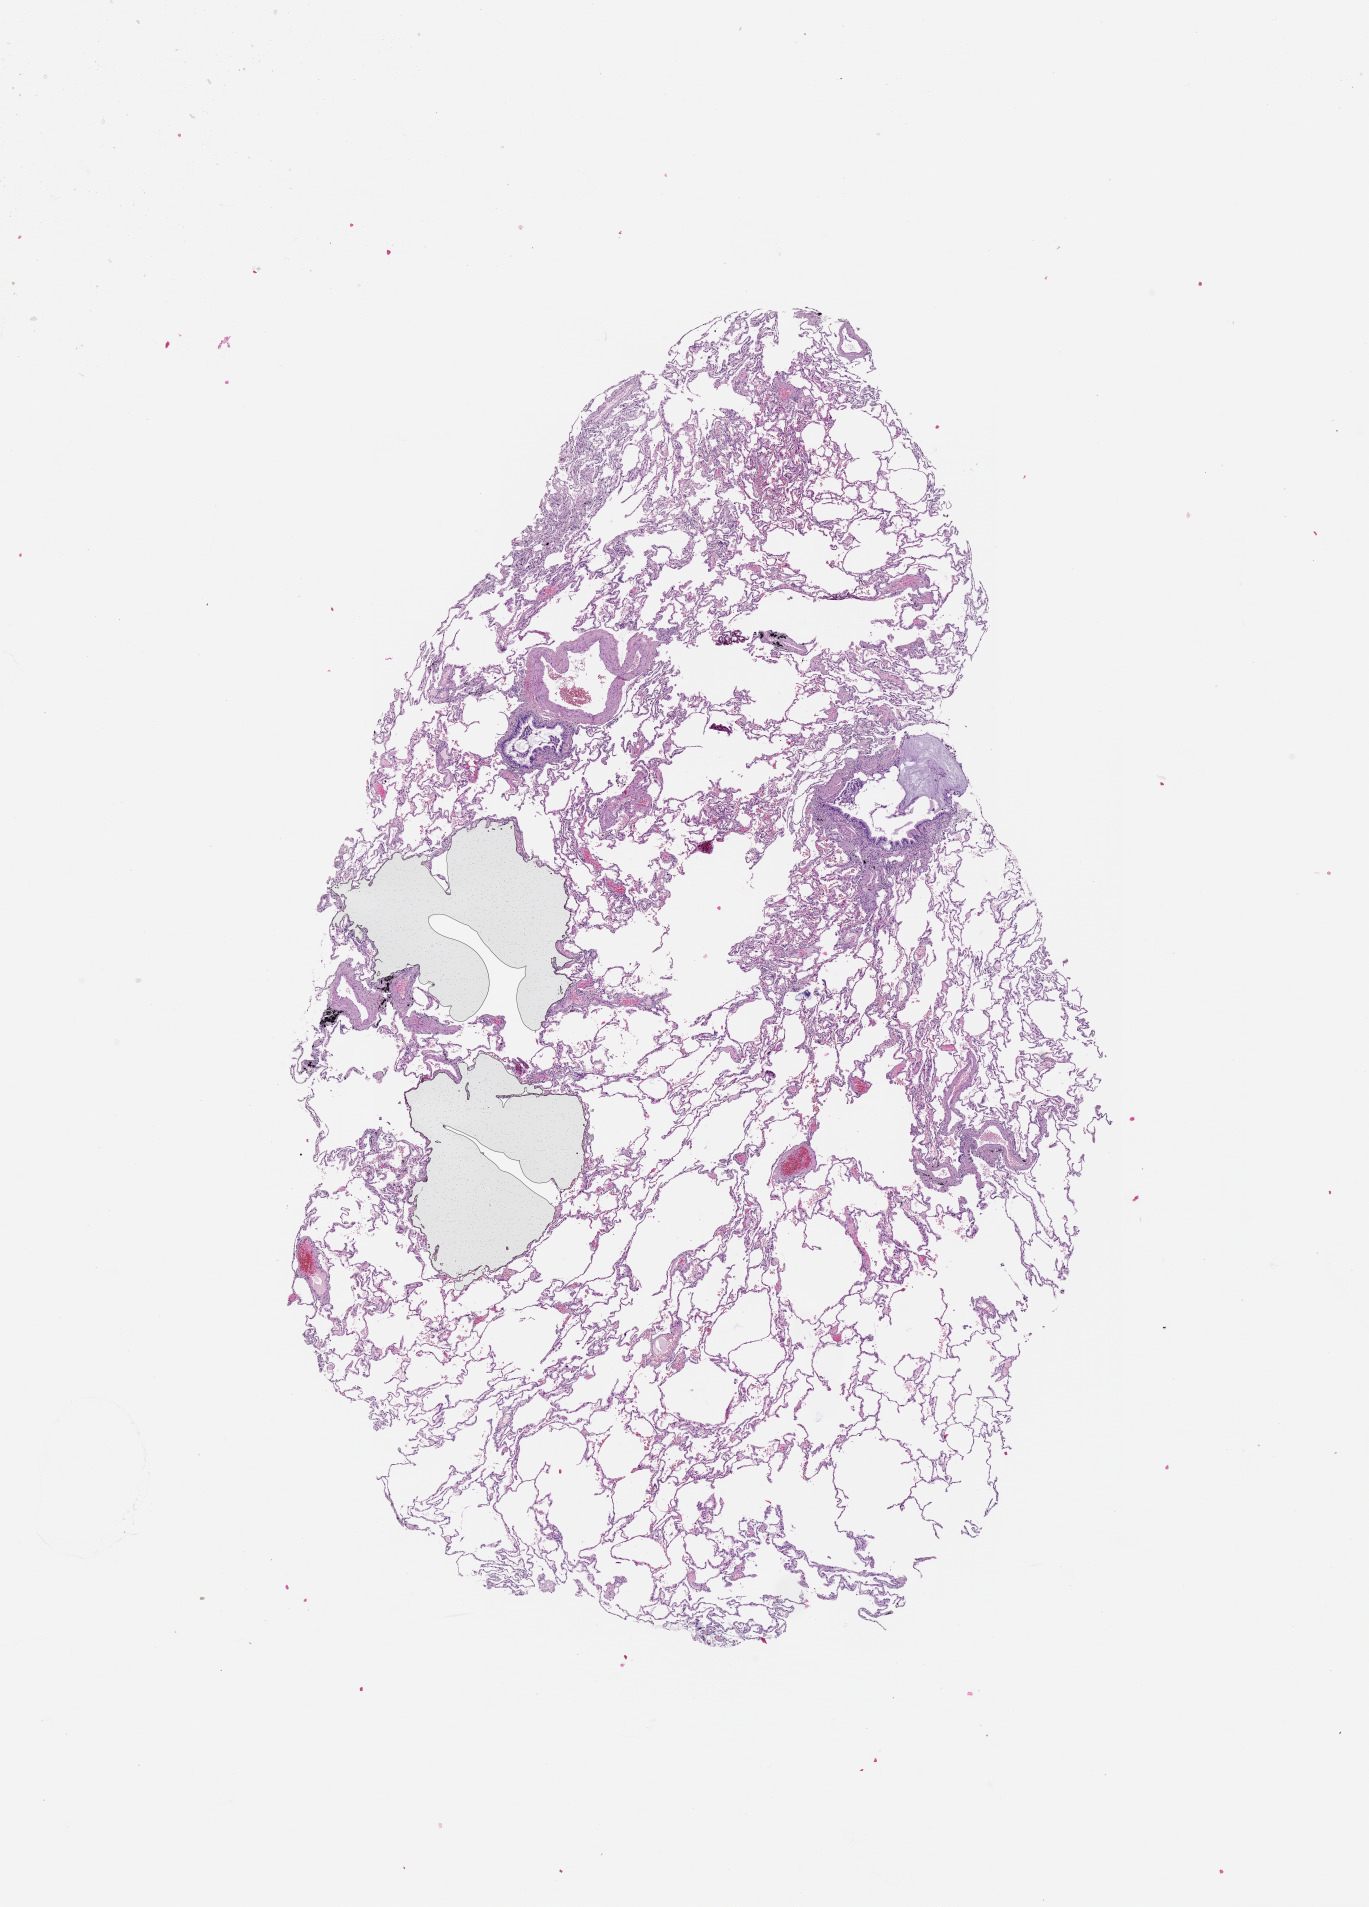
Whole-slide histology image, H&E — low-resolution overview of the scanned area, about 11.0 x 15.4 mm (slide scanned at 20x); lung, normal (non-tumour) tissue. 67-year-old male patient.
This section: normal (non-tumour) tissue from the same patient. Patient diagnosis (cohort enrolment): squamous cell carcinoma (lung).